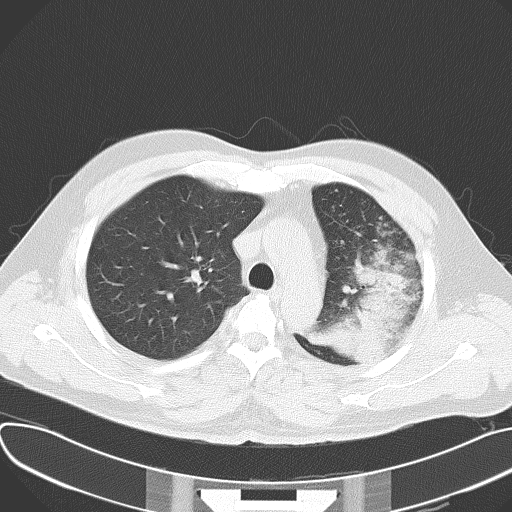
Chest CT, one axial slice; 120 kVp; lung window (W 1500 / L -600 HU); 5 mm slice thickness; 512 × 512 image matrix. Patient: male, 48 years. Case-level facts recorded for this patient, not image findings: clinical TNM (as recorded): T4 N0 M0.
Annotated regions visible in this slice (rectangle marked by the reading radiologist):
- lung tumour (recorded histology: adenocarcinoma): bounding box <320,258,407,376> (left, top, right, bottom; pixels)